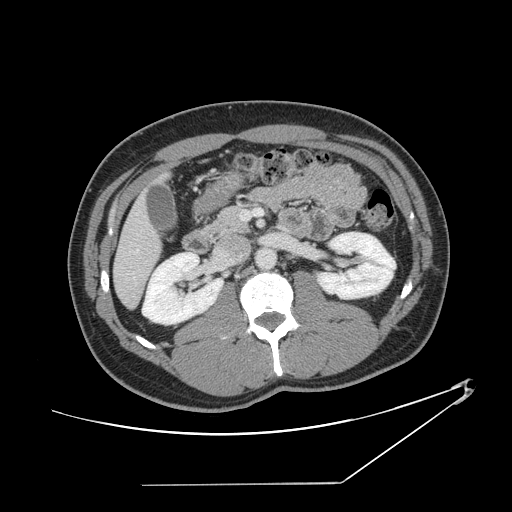
Contrast-enhanced abdominal CT, one axial slice. Reconstruction kernel STANDARD. Intravenous contrast given. Soft-tissue window (W 400 / L 40 HU). 2.5 mm slice thickness. 512 × 512 image matrix, field of view 432 × 432 mm. Male patient, age 45 years. From the clinical record (not read from this slice): diagnosis: colorectal cancer liver metastases, imaged before liver resection; multiple liver metastases: no; largest metastasis: 1 cm; disease in both lobes: no.
Annotated regions visible in this slice (manually delineated by an expert):
- hepatic veins: bounding box (x1, y1, x2, y2) in pixels: (130, 248, 140, 254)
- liver: (115, 200, 160, 307)
- planned liver remnant (the part of the liver to remain after resection): (115, 199, 161, 307)
- portal vein (with intrahepatic branches): (241, 209, 263, 220)